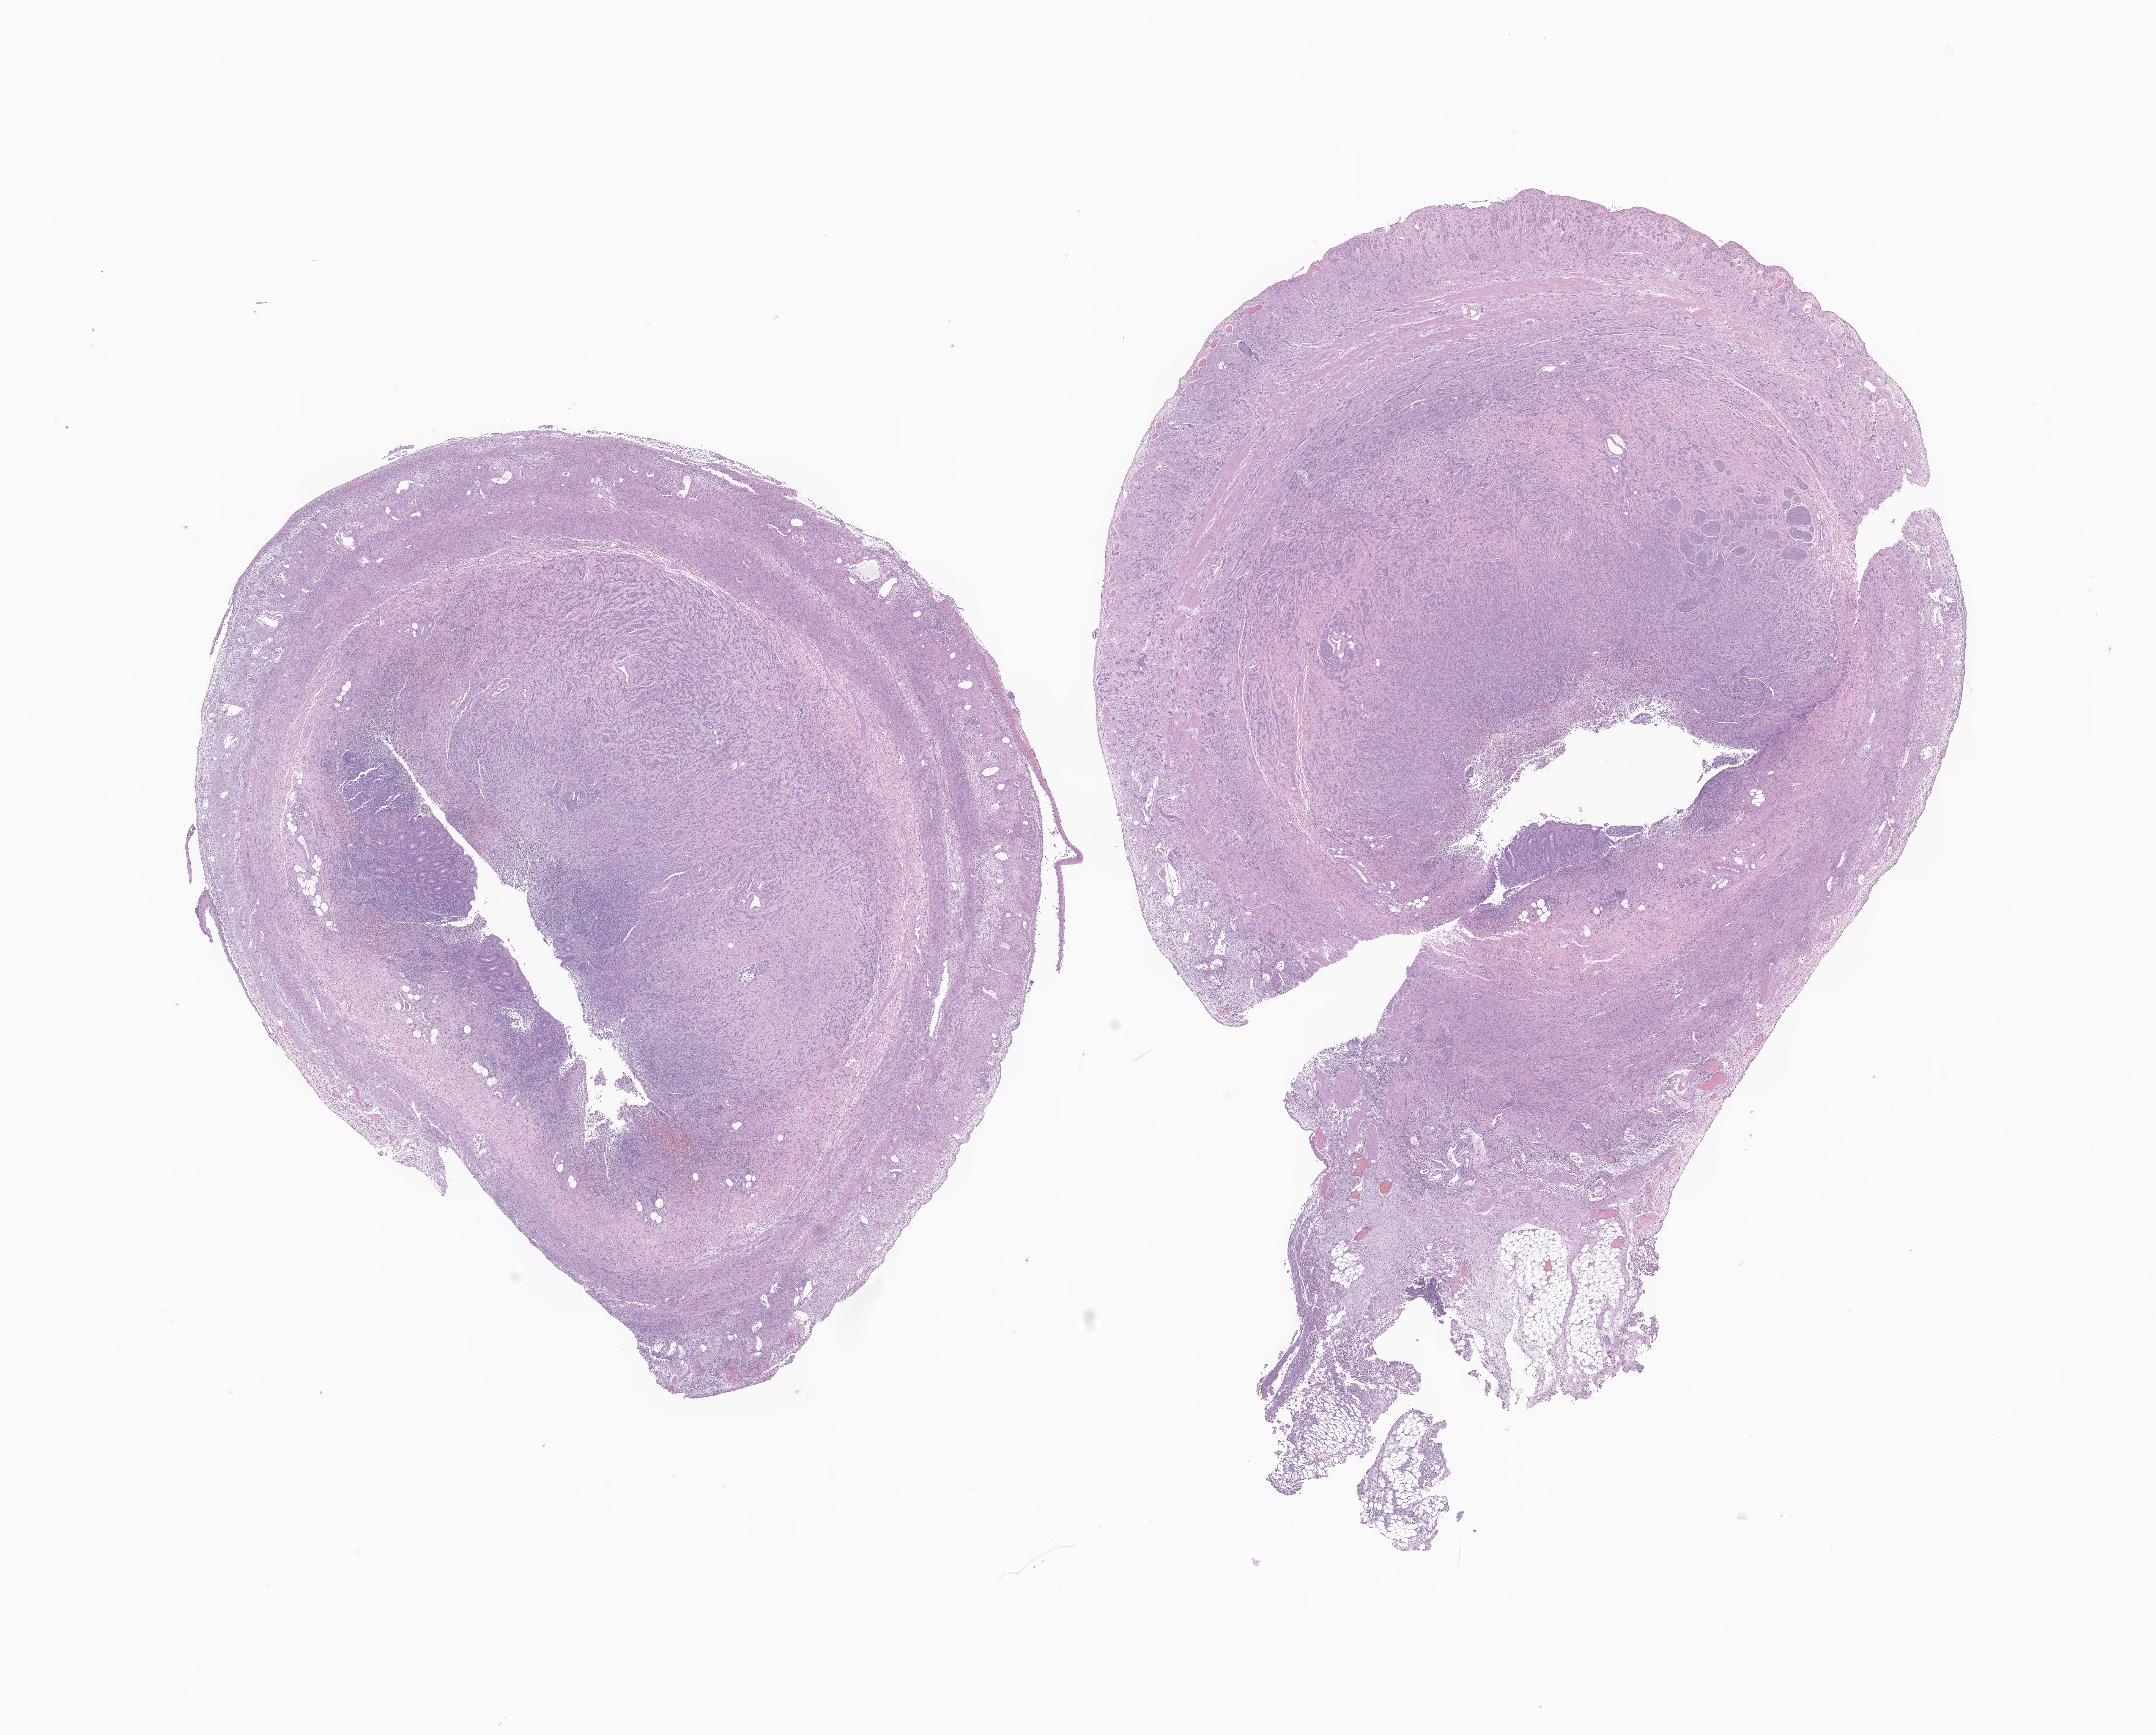
H&E whole-slide image of tumor tissue from the appendix, low-resolution overview of the scanned area, about 21.5 x 17.3 mm. FFPE section. Female patient, age 148 months (12 years 4 months).
- recorded diagnosis: Neuroendocrine carcinoma, NOS